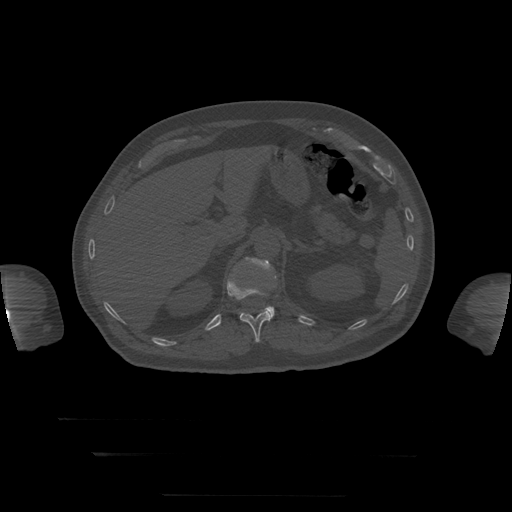
CT including the spine, one axial slice. Slice 66 of 397 in the series (ordered by position). Reconstruction kernel STANDARD. Bone window (W 1800 / L 400 HU). 1.25 mm slice thickness. 512 × 512 image matrix, field of view 510 × 510 mm. Patient age 73 years. From the clinical record (not read from this slice): primary cancer: prostate.
Outlined on this slice (semi-automatically segmented with operator editing):
- L1 vertebra: bounding box <241,258,275,319> (left, top, right, bottom; pixels)
- T12 vertebra: <227,279,271,343>